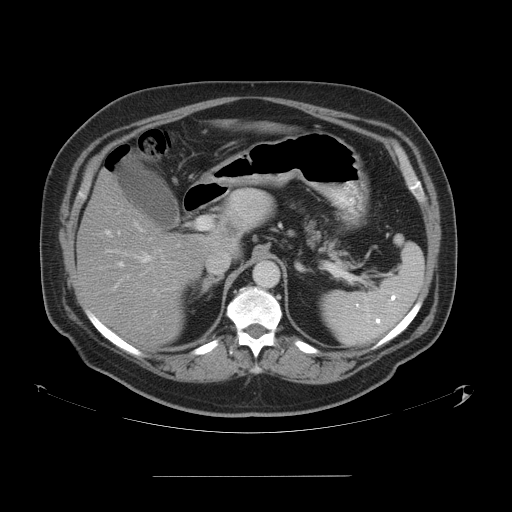
Contrast-enhanced abdominal CT, one axial slice. Position 33 of 58 along the scan axis. Intravenous contrast given. Soft-tissue window (W 400 / L 40 HU). 5 mm slice thickness. 512 × 512 image matrix, field of view 480 × 480 mm. Male patient, age 63 years. Case-level facts recorded for this patient, not image findings: diagnosis: colorectal cancer liver metastases, imaged before liver resection; multiple liver metastases: no; largest metastasis: 4.2 cm; disease in both lobes: no.
Structures marked on this image (outlined manually by an expert reader):
- hepatic veins: bounding box [x1, y1, x2, y2] px = [114, 256, 165, 288]
- liver: [78, 174, 271, 344]
- planned liver remnant (the part of the liver to remain after resection): [78, 190, 202, 344]
- portal vein (with intrahepatic branches): [105, 221, 200, 293]
- liver metastasis: [220, 221, 241, 251]